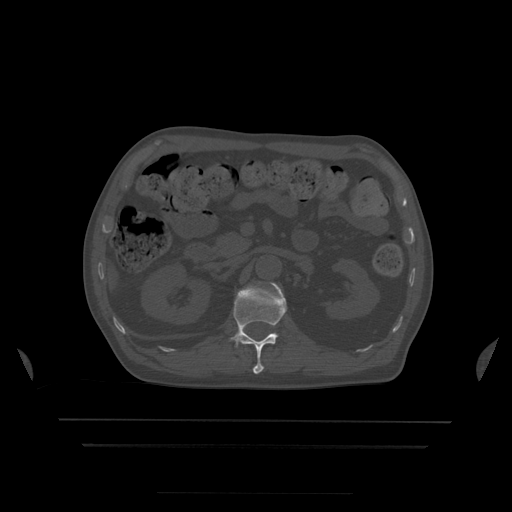
CT including the spine, one axial slice; slice 168 of 522 in the series (ordered by position); bone window (W 1800 / L 400 HU); 1.25 mm slice thickness; 512 × 512 image matrix, field of view 436 × 436 mm. Patient age 68 years. From the clinical record (not read from this slice): primary cancer: urothelial.
Structures marked on this image (semi-automatic segmentation, software-assisted and operator-edited):
- L1 vertebra: bounding box [x1, y1, x2, y2] px = [230, 284, 287, 375]